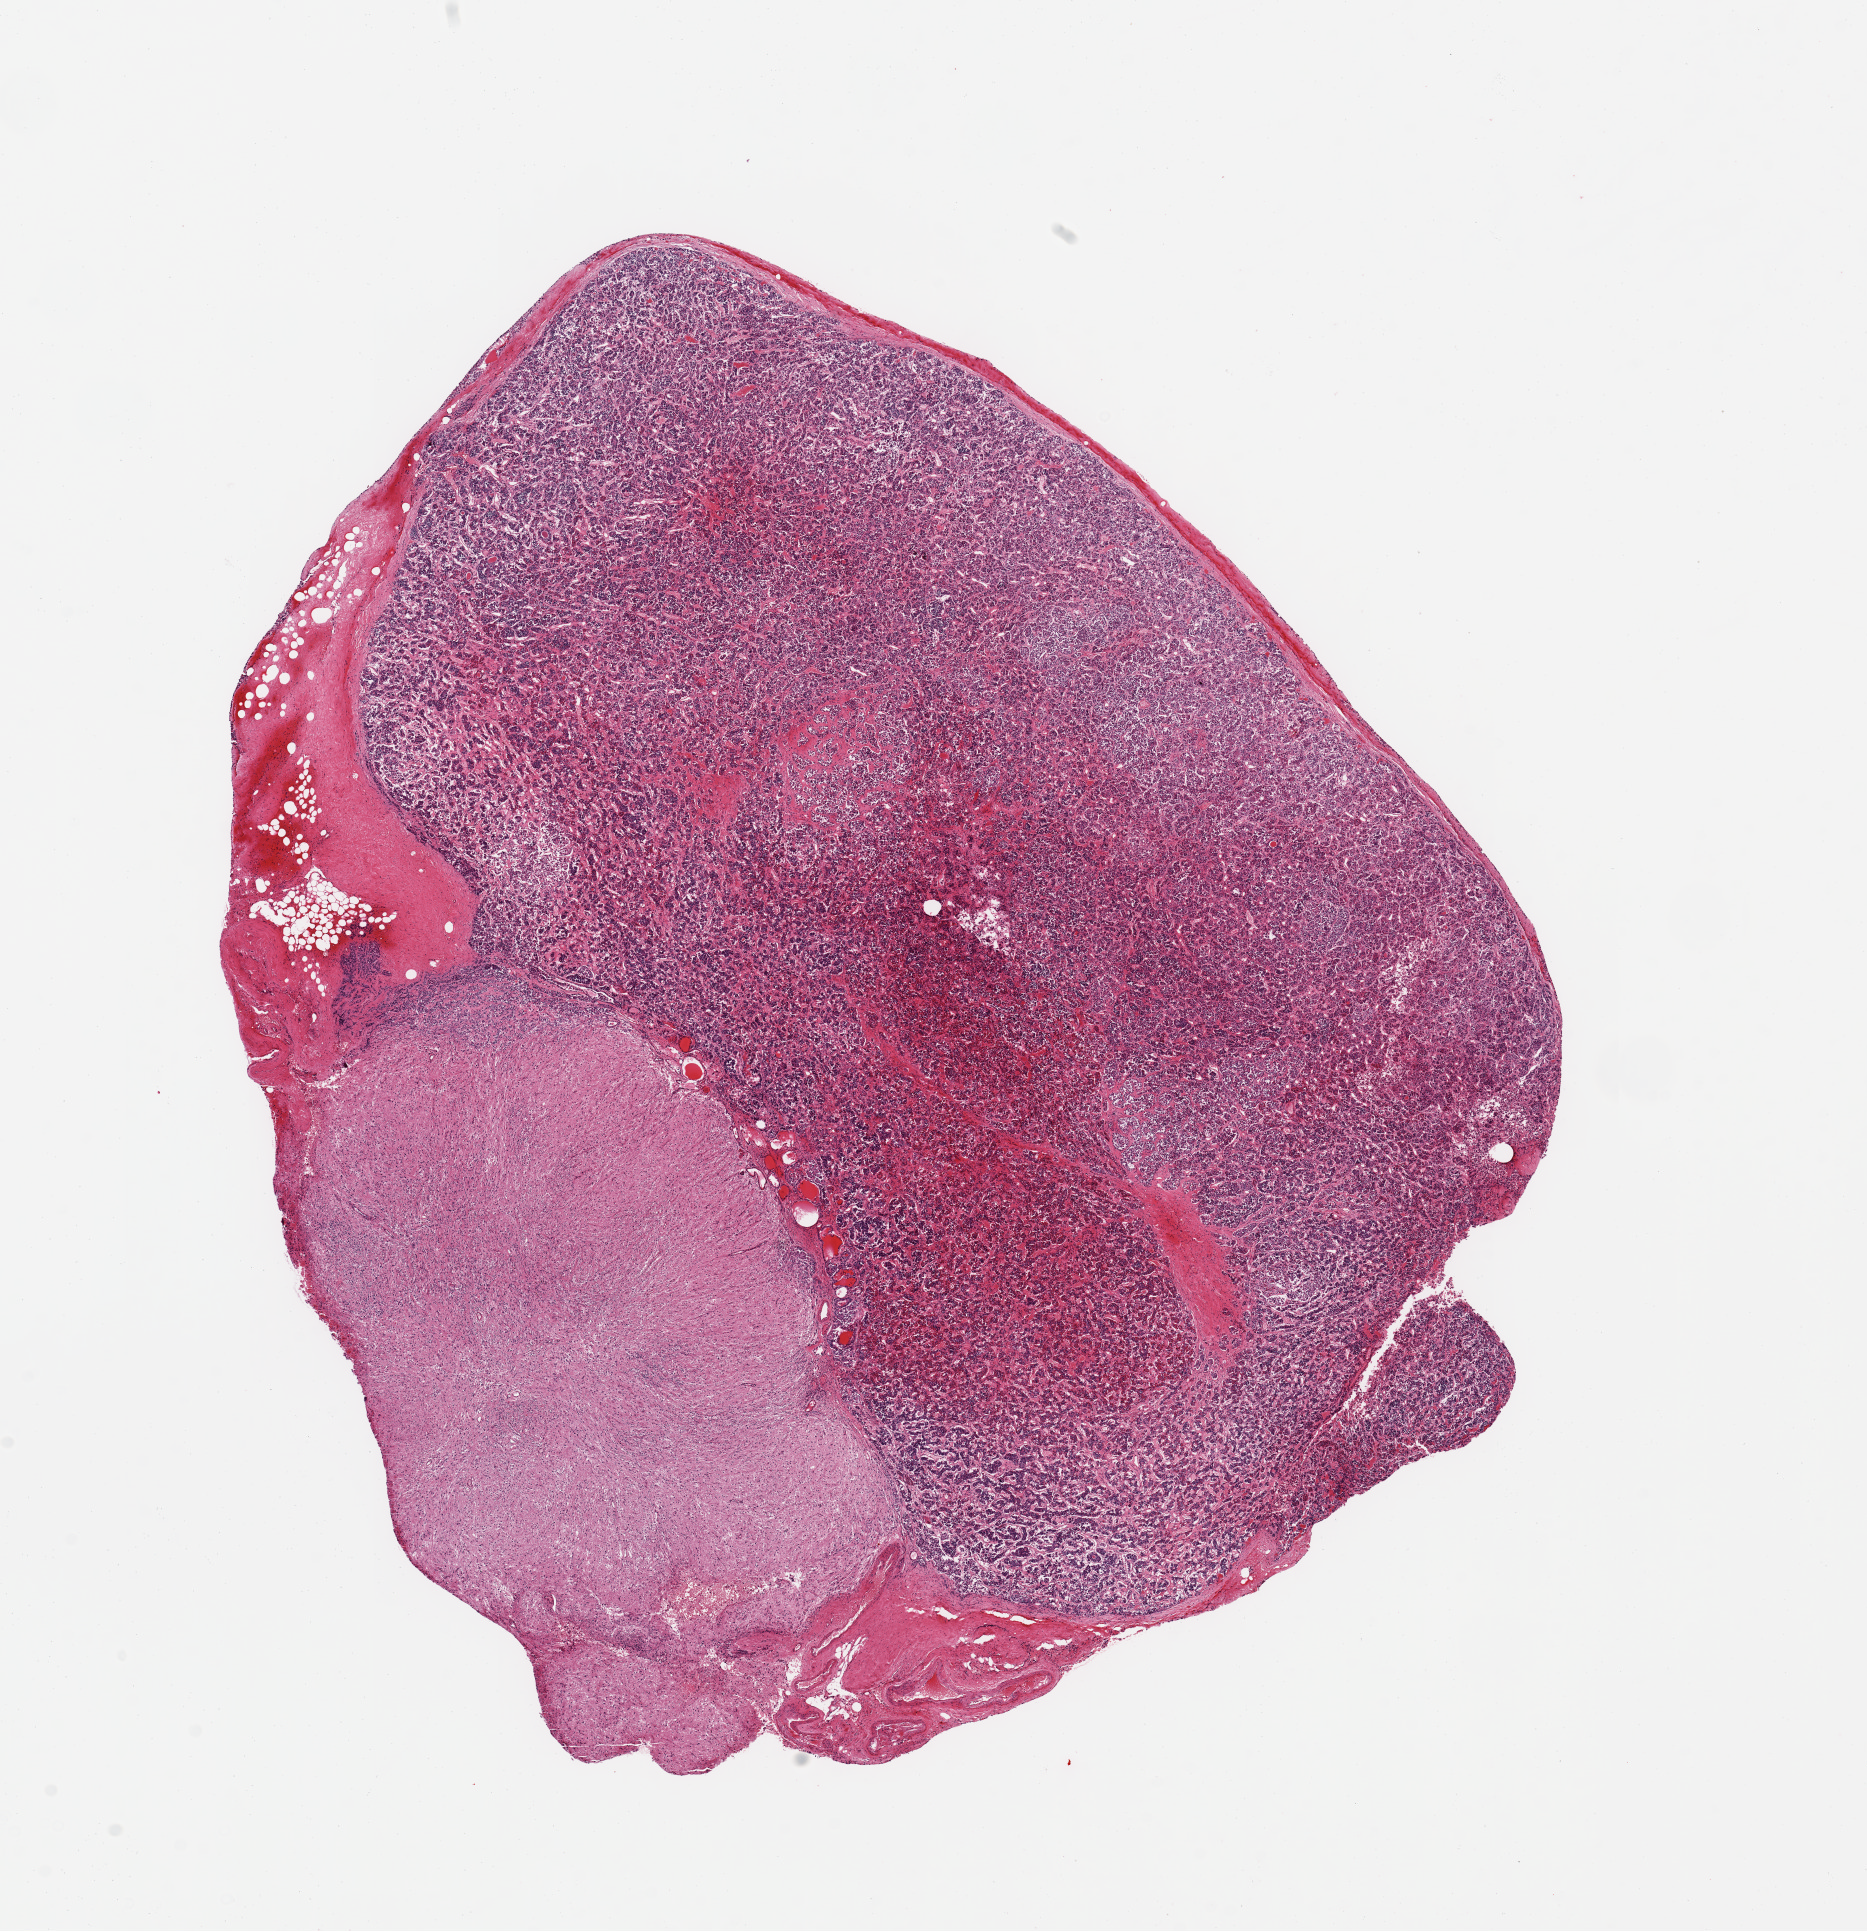
Digitized H&E-stained section, brightfield, shown as a low-resolution overview of the whole scanned area (about 14.8 x 15.3 mm), PAXgene-fixed, paraffin-embedded tissue, target tissue: pituitary, tissue donor sample. Donor: male.
Reviewer comment on this tissue sample: 1 piece; mainly adenohypophysis; ~6x3.5mm nubbin of neurohypophysis.